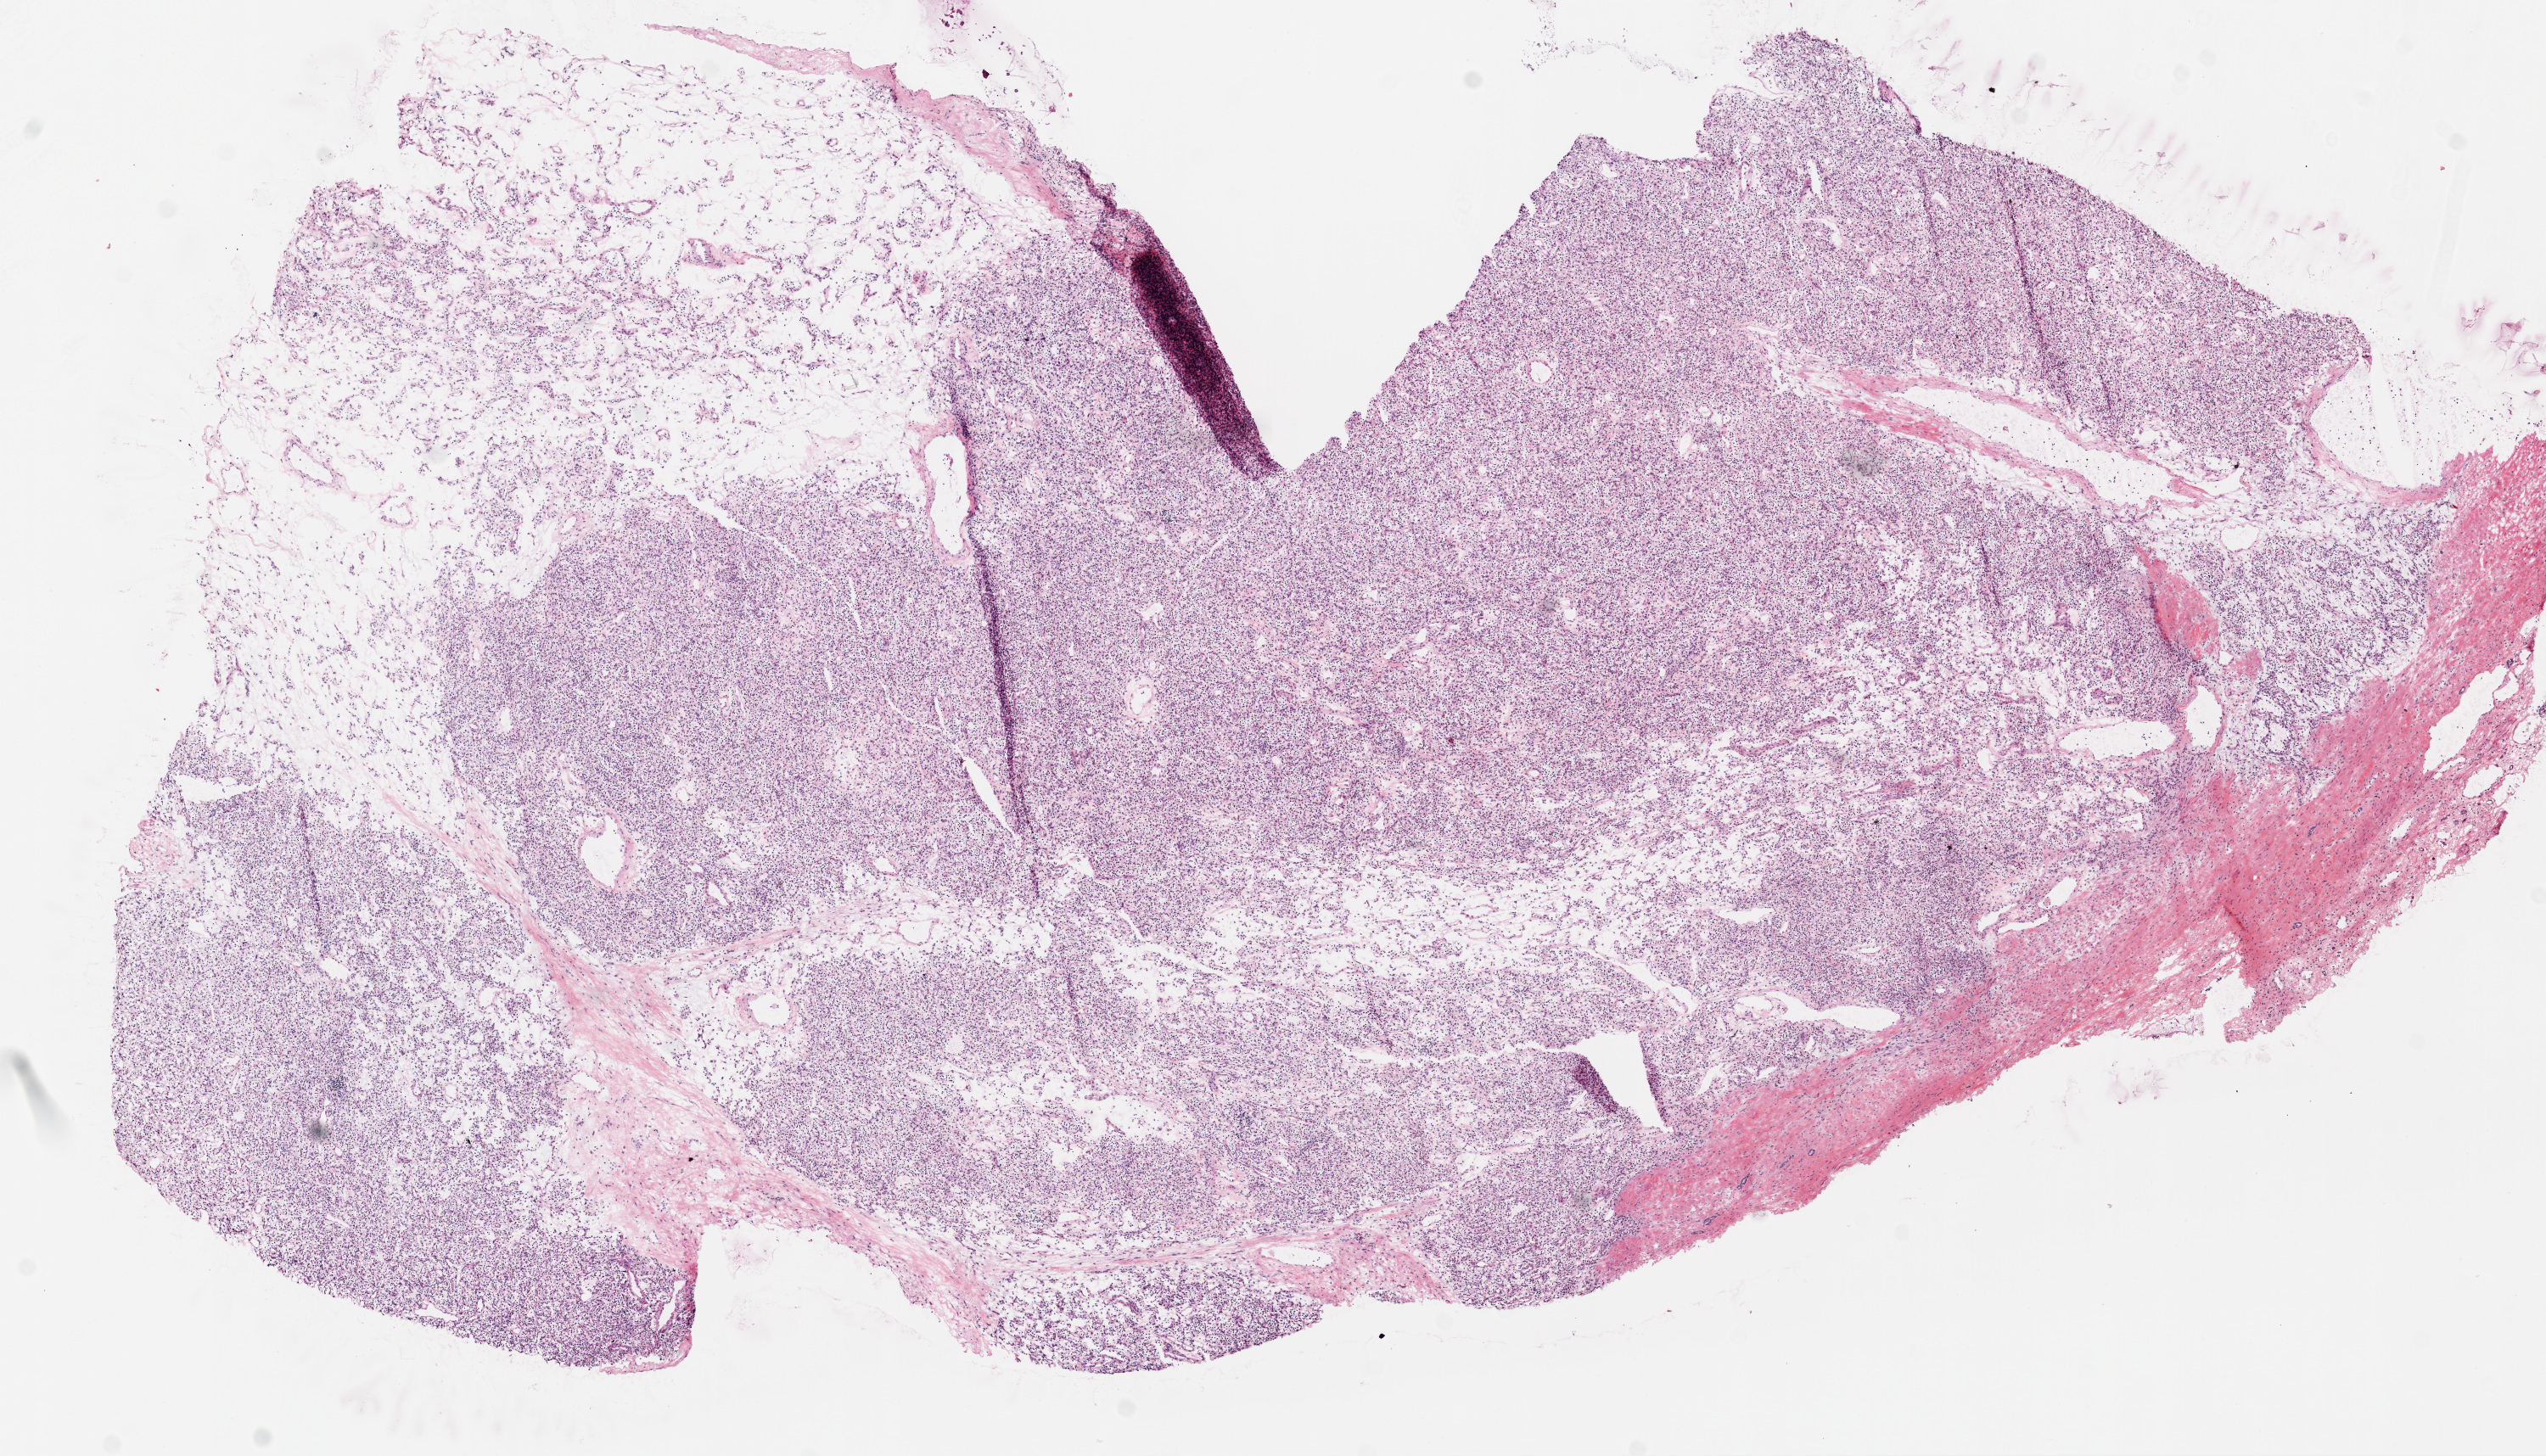
Whole-slide histology image, H&E-stained, whole scanned area (about 12.0 x 6.9 mm, slide scanned at 20x) shown as a low-resolution overview; frozen section from the top of the tissue portion; kidney, primary tumour sample. Male patient; age at initial diagnosis 59 years. Histologic grade: G1 (well differentiated). Slide review estimates, as recorded: tumour cells 90%, tumour nuclei 85%, normal cells 0%, stromal cells 10%, necrosis 0%. Infiltration values recorded for this section: lymphocyte infiltration 3%, monocyte infiltration 0%, neutrophil infiltration 0%.
AJCC pathologic stage: I (7th edition). Pathologic diagnosis: Clear cell adenocarcinoma, NOS. TNM: T1 N0 M0. Laterality: right.